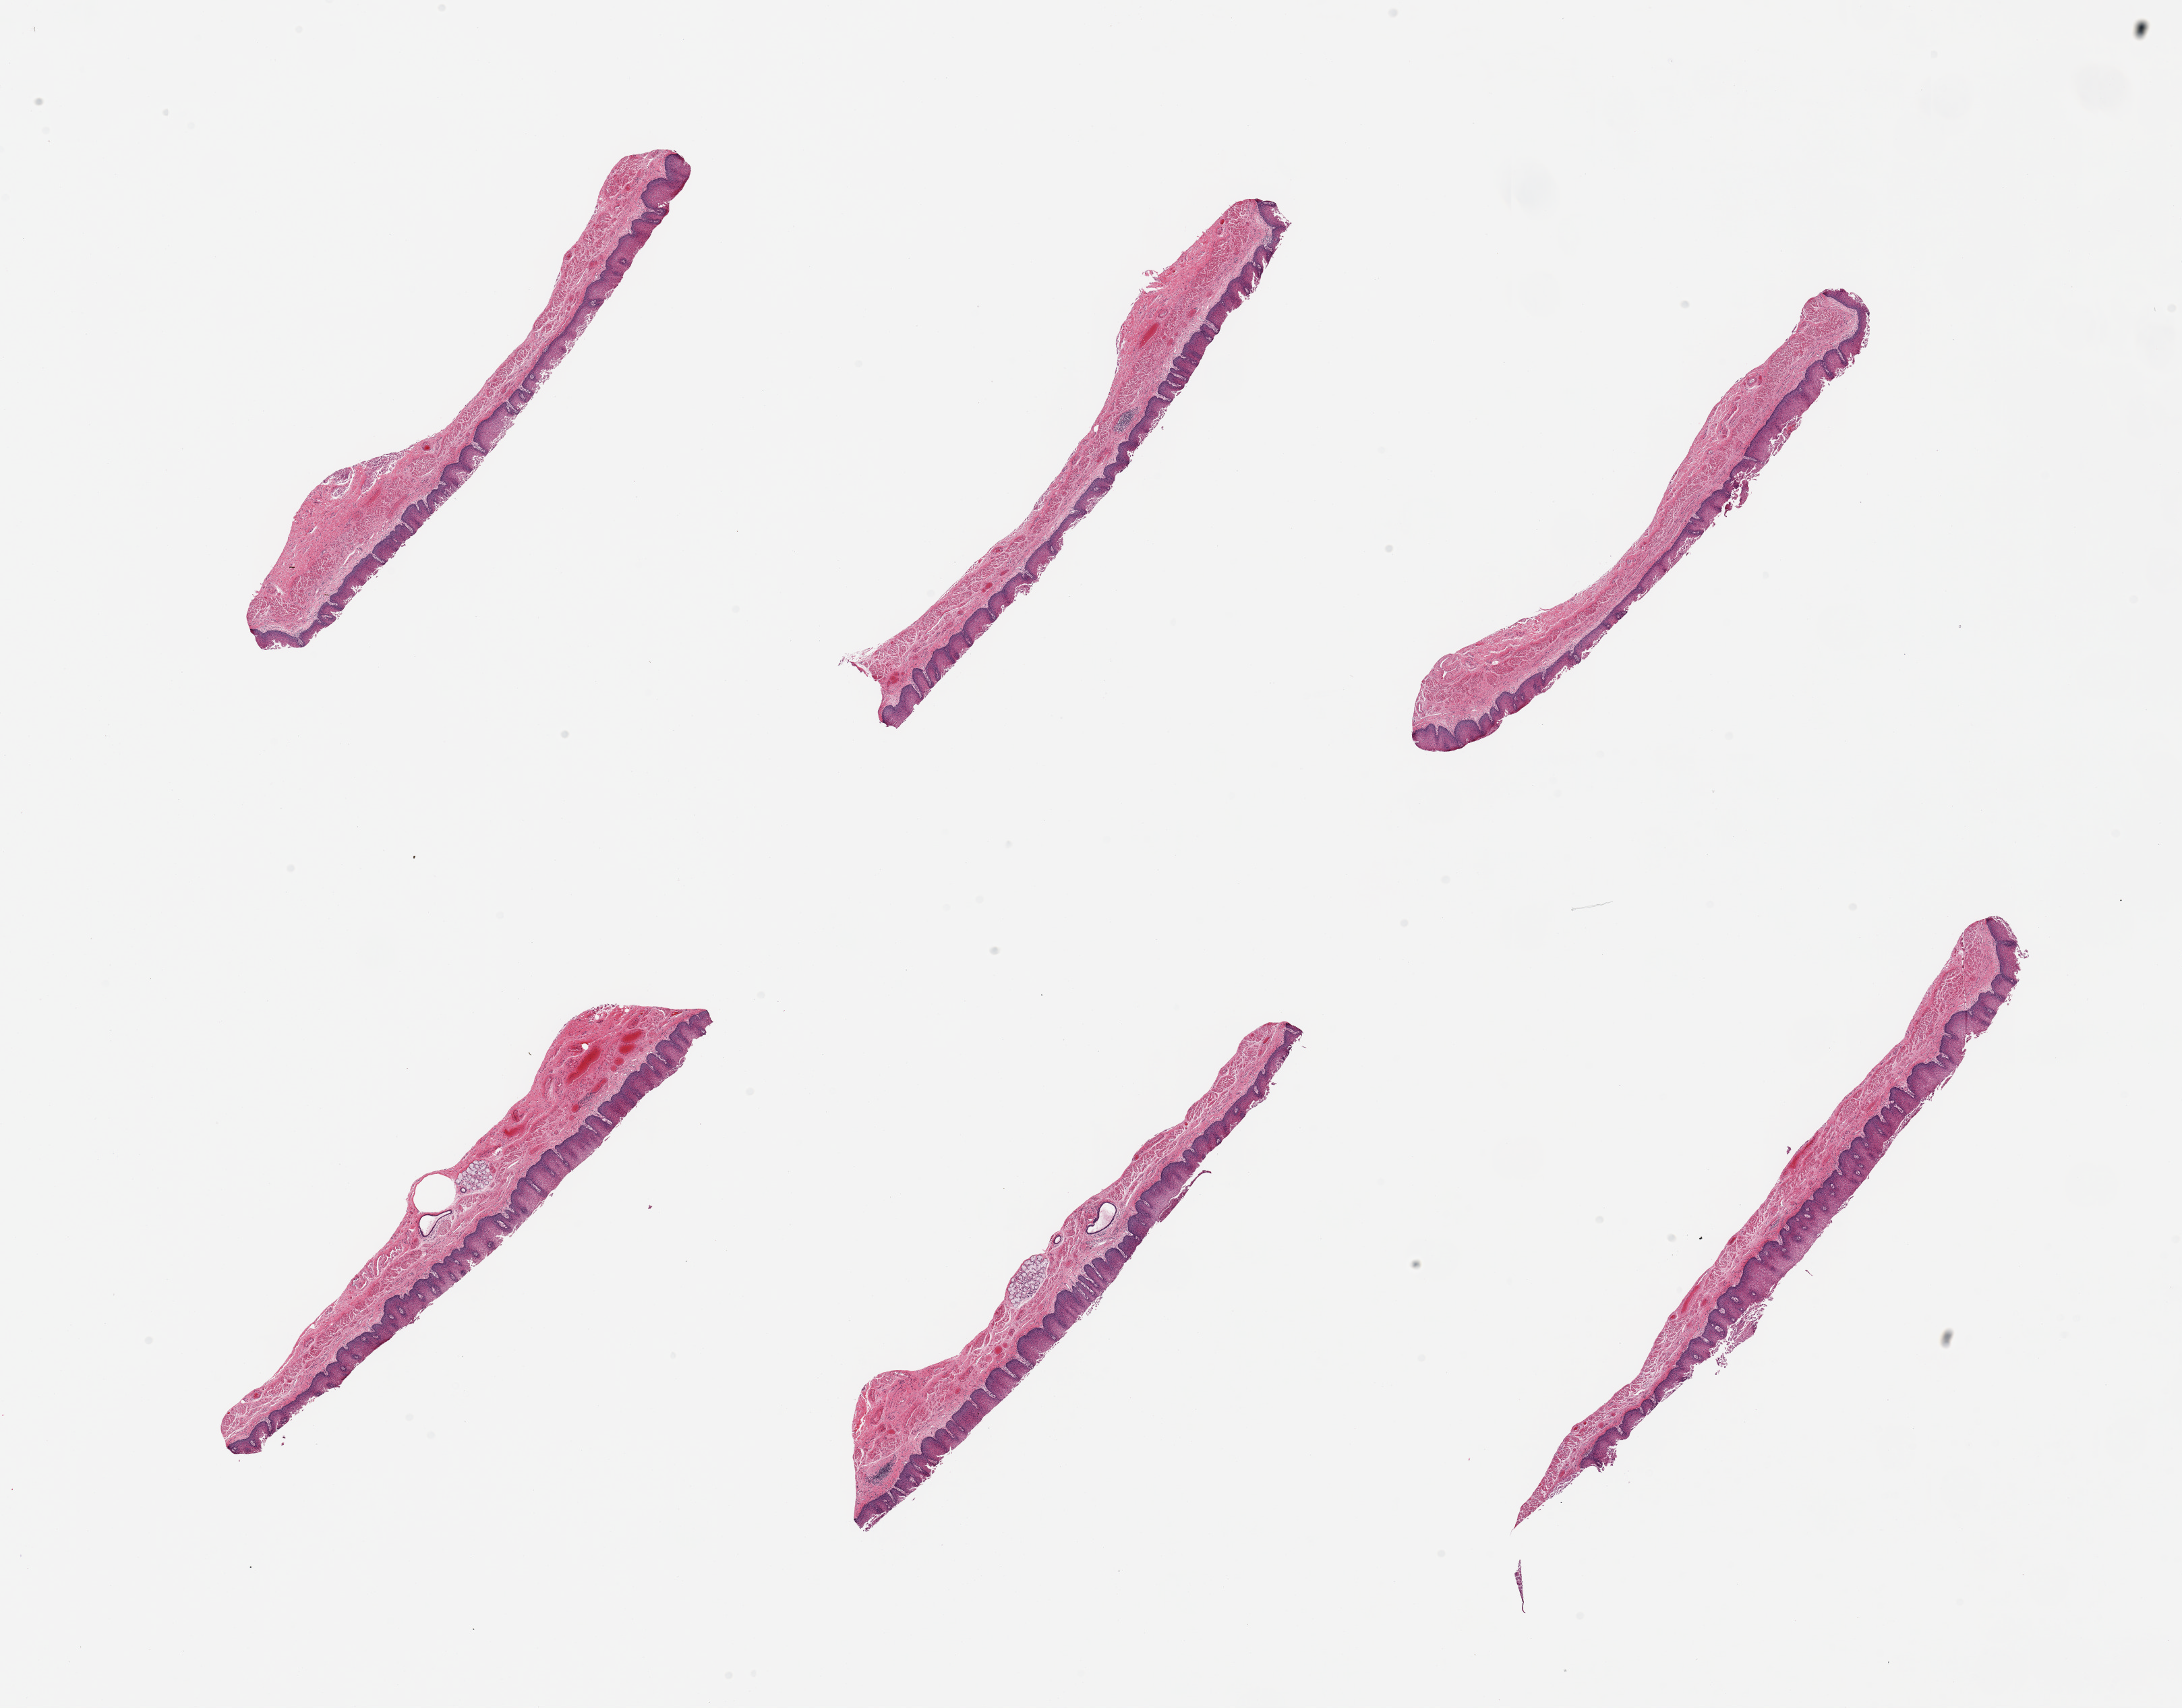
Digitized H&E-stained section — shown as a low-resolution overview of the whole scanned area (about 25.6 x 20.0 mm, from a 20x scan). PAXgene-fixed paraffin-embedded (PFPE) section. Target tissue: esophageal mucous membrane. Tissue donor sample. Donor sex: female.
Reviewer comment on this tissue sample: 6 pieces; partially sloughed epithelium.